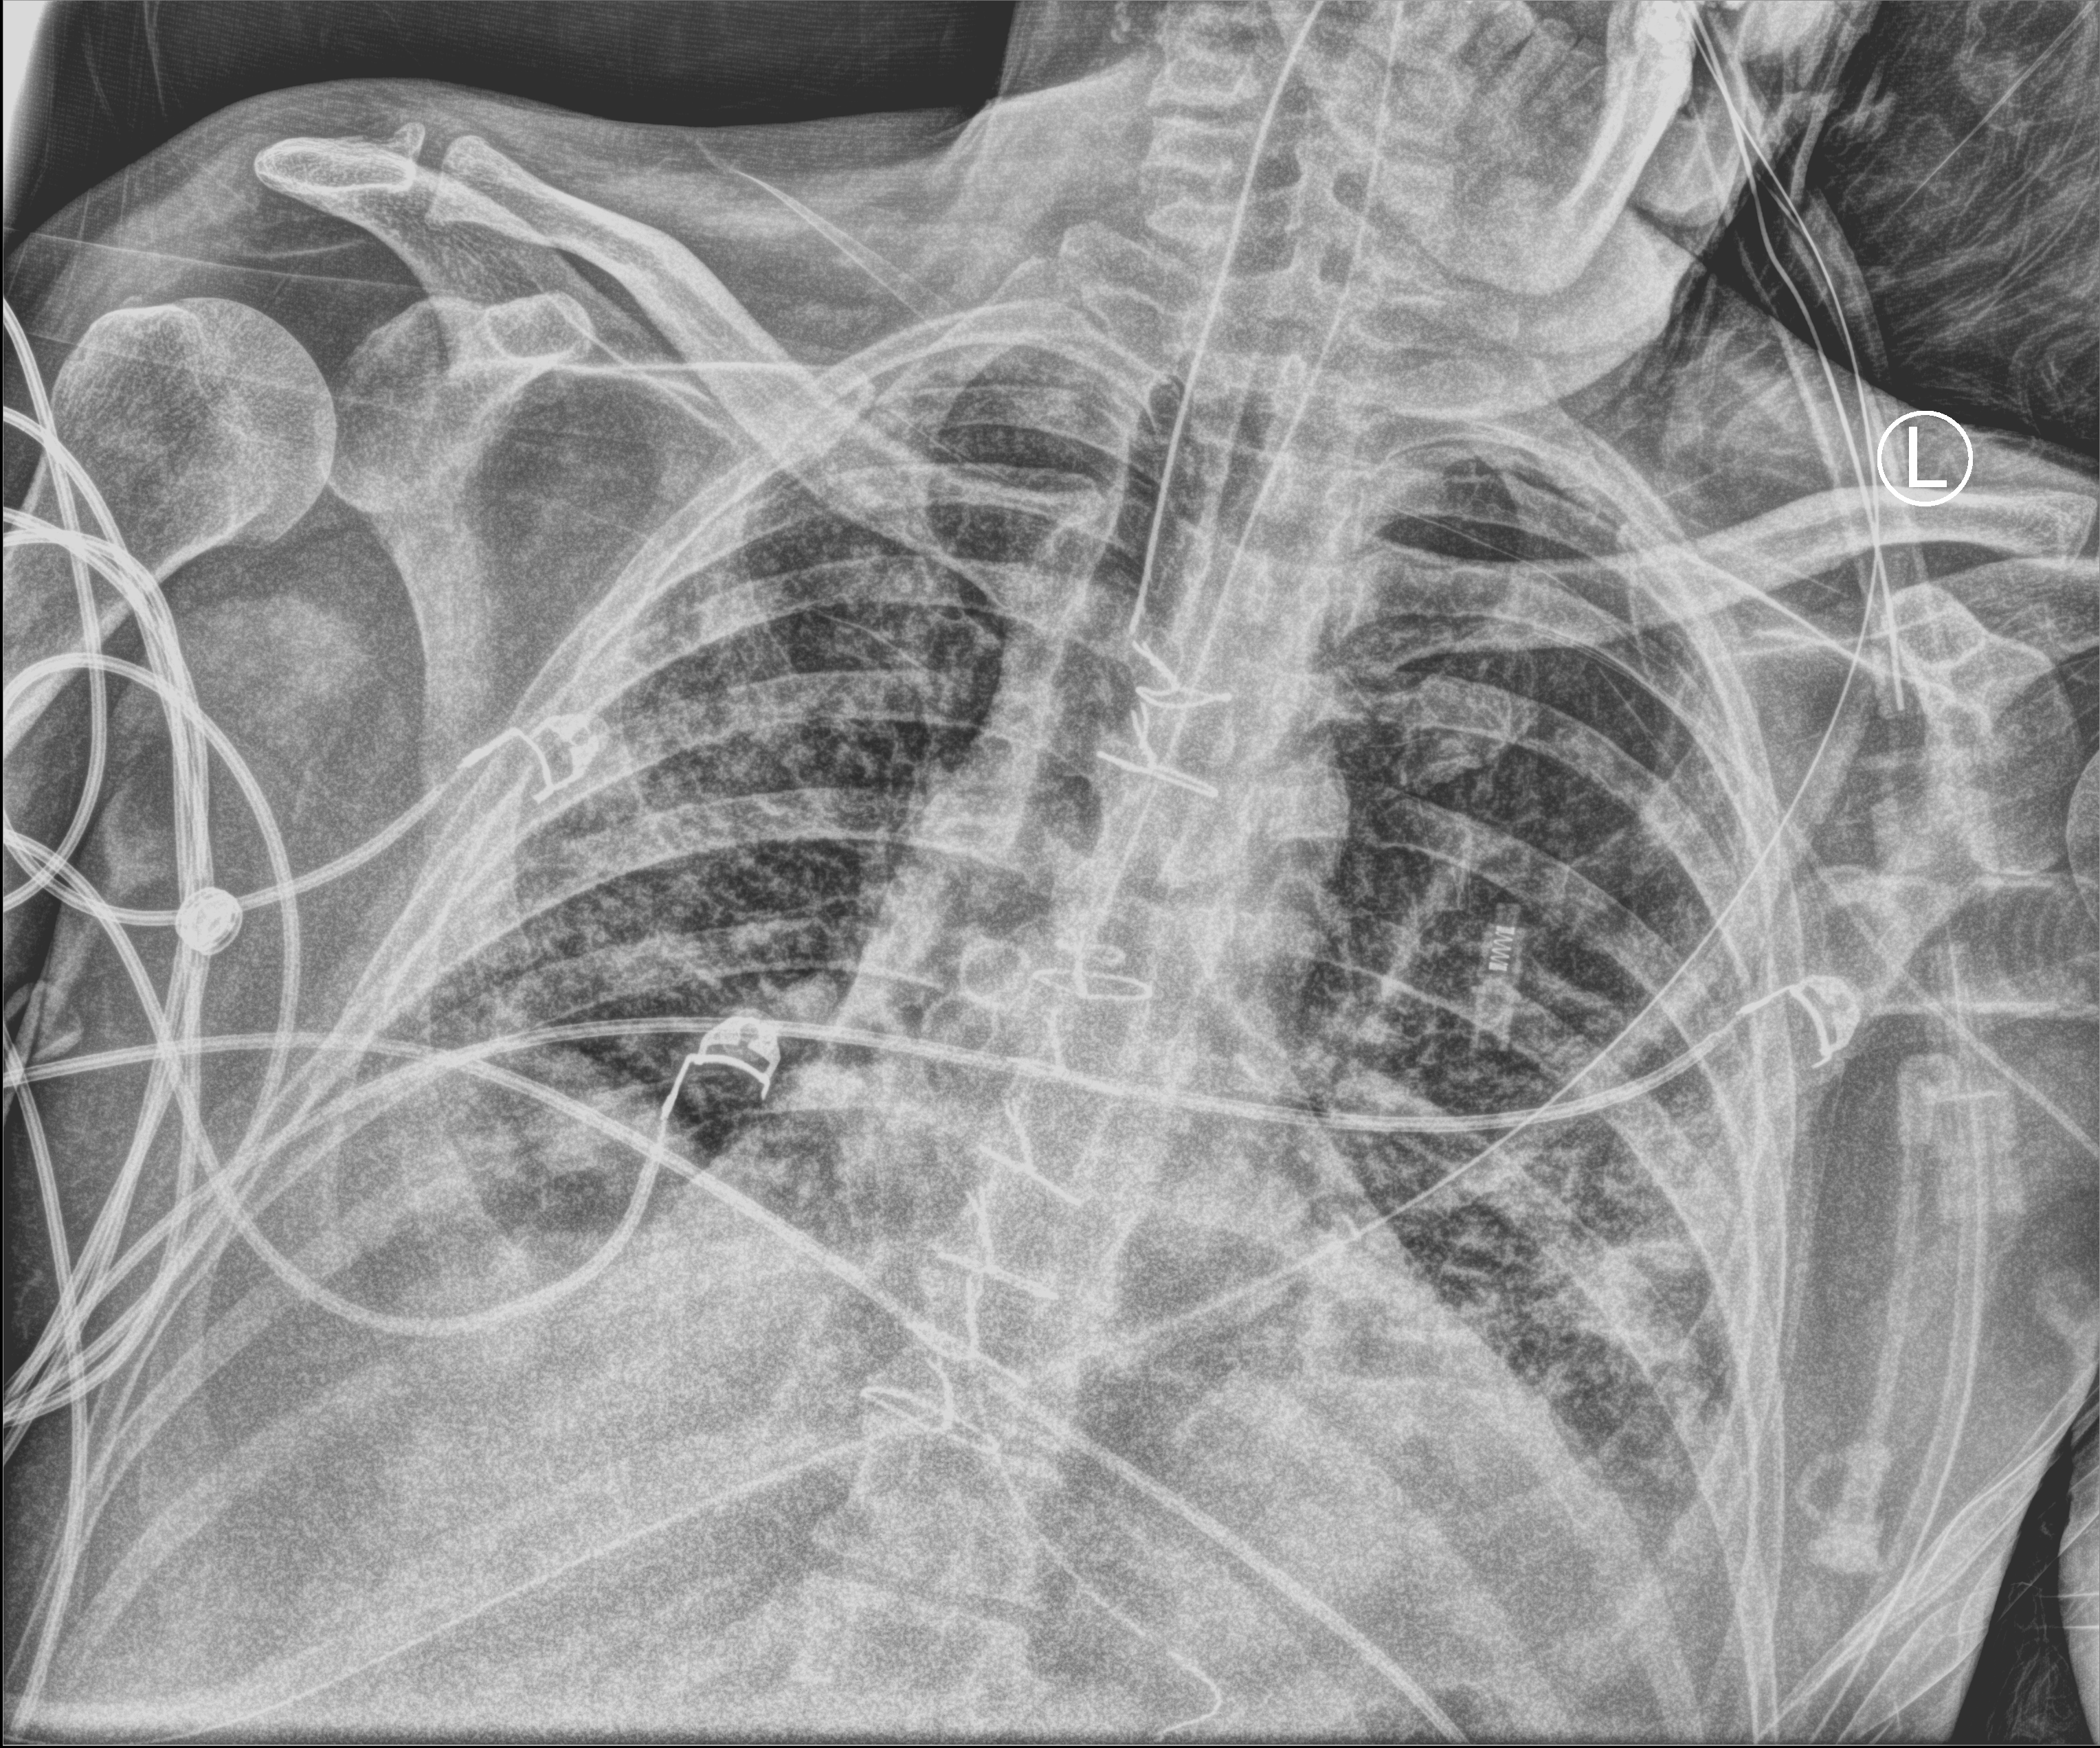
Portable chest radiograph, anteroposterior (AP) projection. Patient hospitalised with COVID-19; male, aged 18–59 years.
Admission-level facts for this patient (not findings on this image; timing relative to this image not recorded): admitted to intensive care during this hospital stay: yes; length of hospital stay: 63 days; mechanically ventilated during this hospital stay: yes.